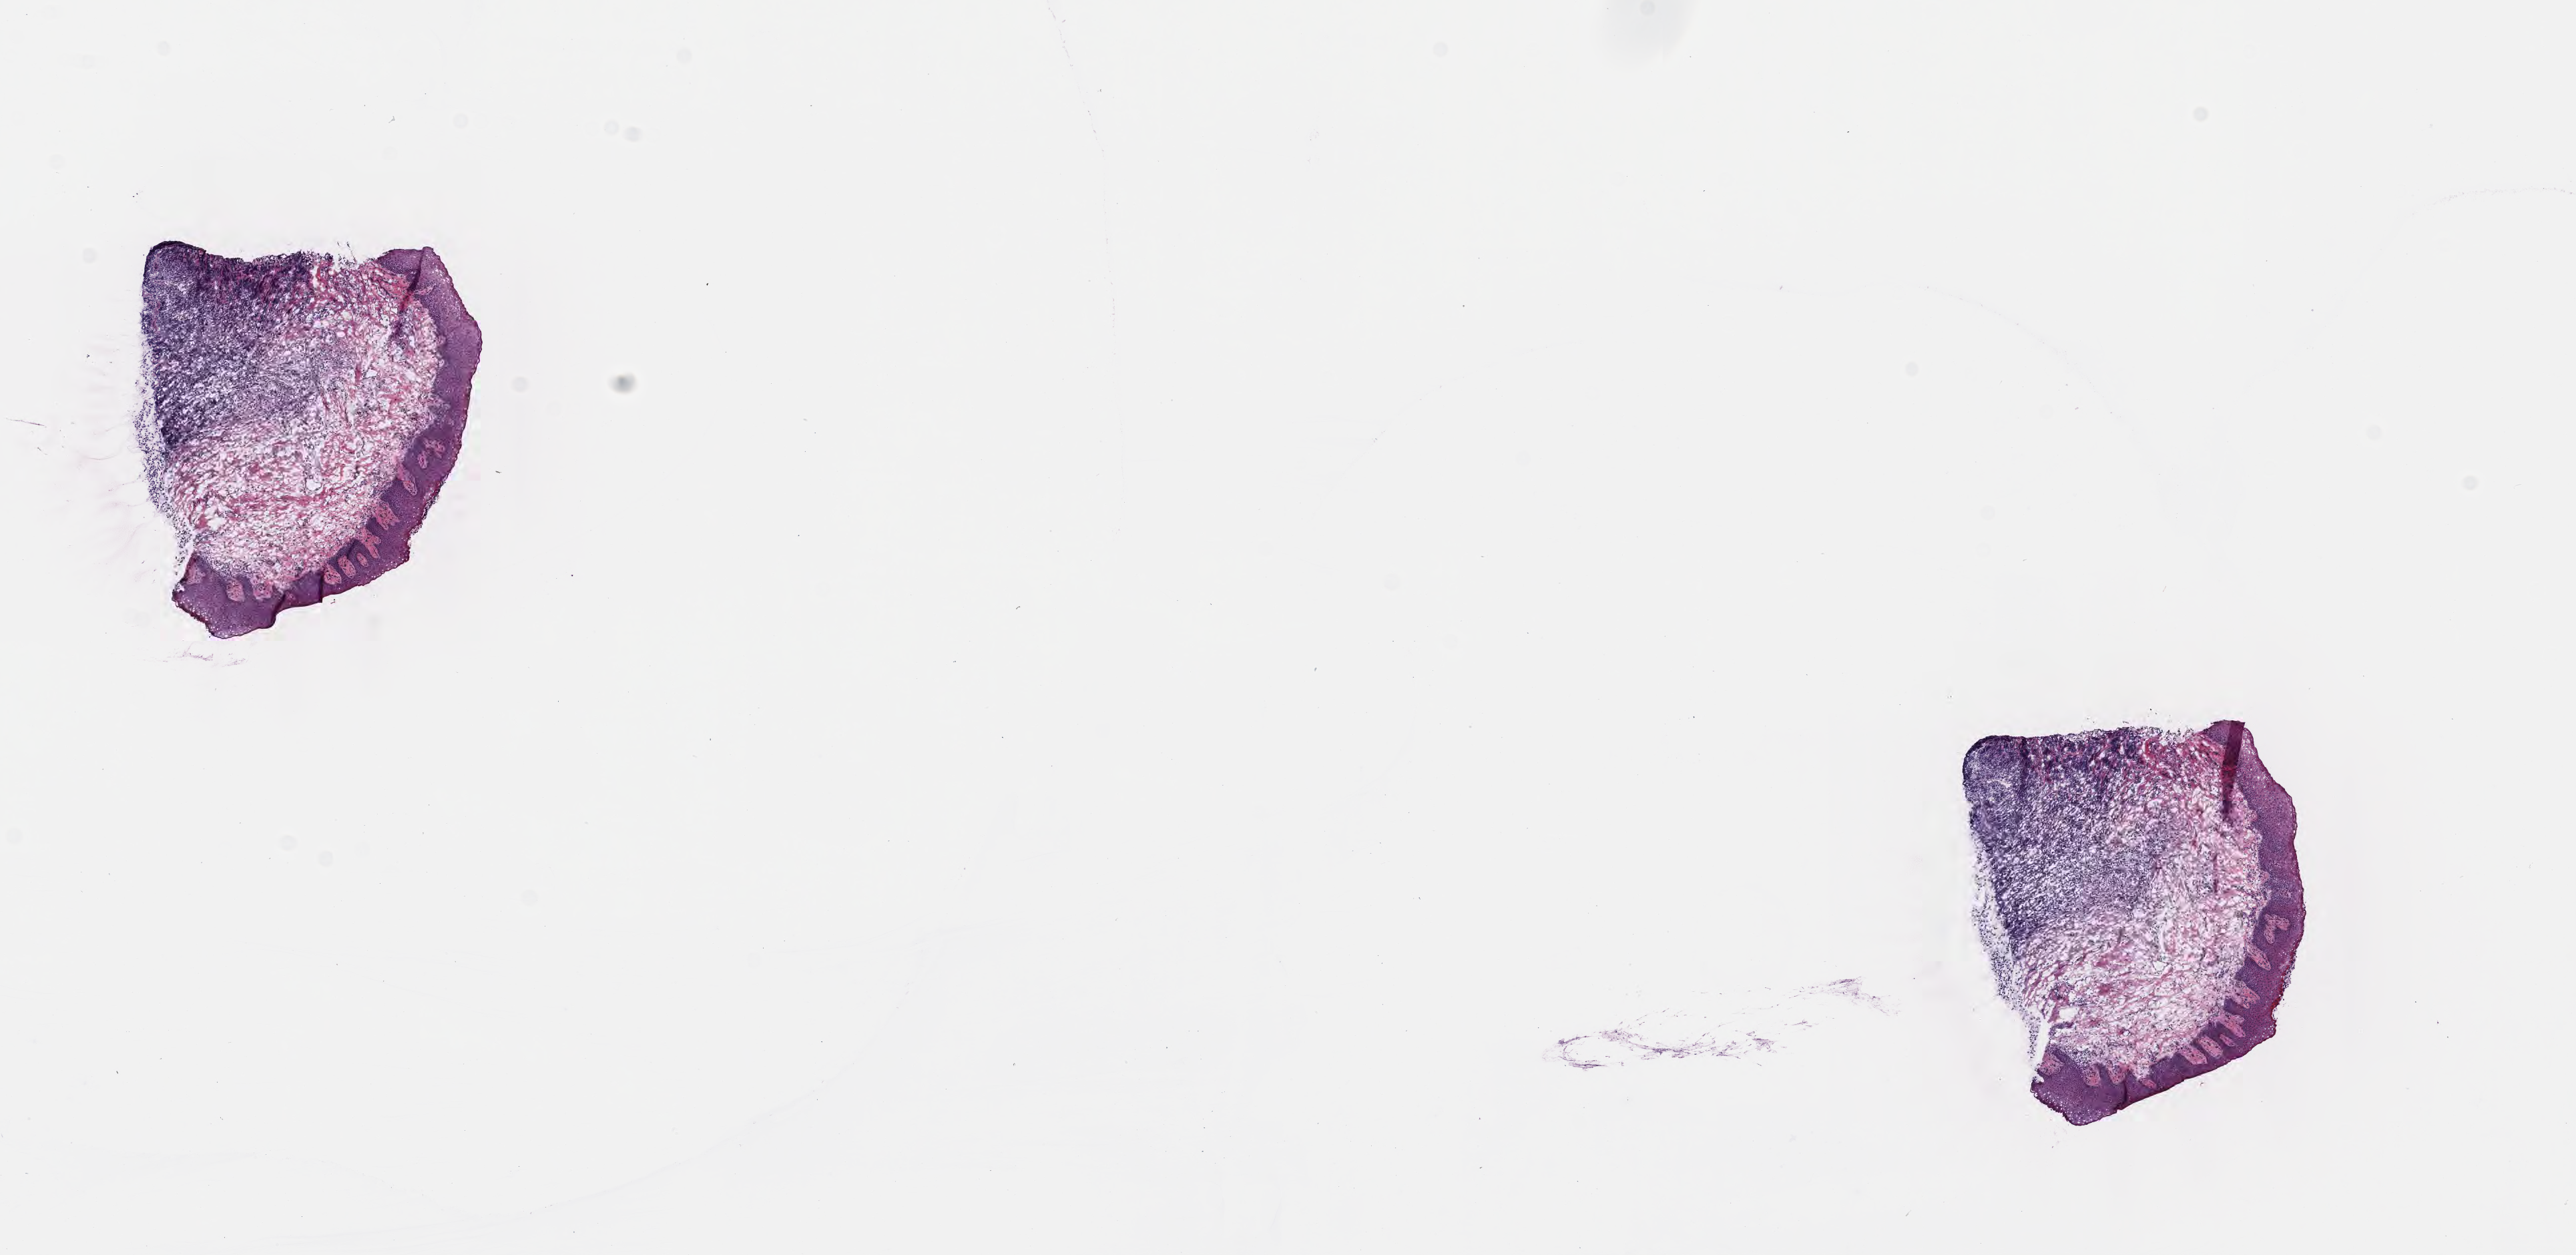
Digitized haematoxylin and eosin-stained section, low-resolution overview of the scanned area, about 15.6 x 7.6 mm; frozen section (tissue freezing medium); primary tumor; site: gum of mandible. Male patient, age 10 years. Composition of this section per pathologist review: tumor cells 30%, tumor nuclei 40%, stromal cells 35%, necrosis 5%, normal cells 30%. Inflammatory infiltration, as recorded: lymphocyte infiltration 20%, monocyte infiltration 10%, neutrophil infiltration 0%.
Ann Arbor stage (patient): Stage IV. Histologic diagnosis: Burkitt lymphoma, NOS.